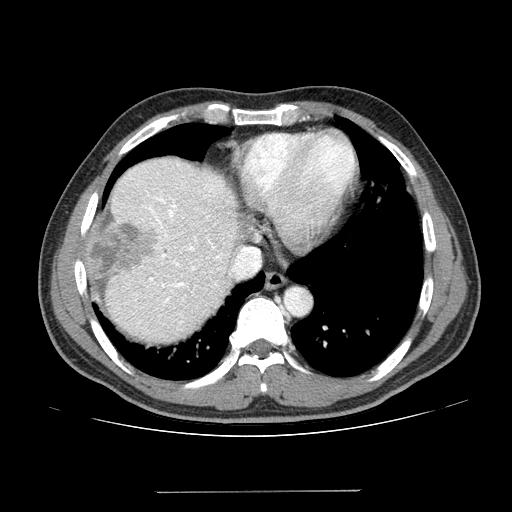
Contrast-enhanced abdominal CT (liver protocol), one axial slice. Position 115 of 131 along the scan axis. Reconstruction kernel STANDARD. 100 kVp. One of 2 acquisitions stored at this slice position. Soft-tissue window (W 400 / L 40 HU). 2.5 mm slice thickness. 512 × 512 image matrix, field of view 380 × 380 mm. Case-level facts recorded for this patient, not image findings: diagnosis: hepatocellular carcinoma (patient treated with transarterial chemoembolisation; whether this scan precedes or follows treatment is not stated here); TNM stage (as recorded): Stage-I; Child-Pugh class: A; tumour differentiation: poorly differentiated; tumour nodularity: uninodular.
Annotated regions visible in this slice (semi-automatically segmented with operator editing):
- liver parenchyma outside the tumour (the mass and vessels are separate outlines, so this box may not span the whole liver): bounding box [x1, y1, x2, y2] px = [84, 156, 238, 342]
- mass: [91, 219, 157, 278]
- liver vessels: [118, 164, 232, 324]